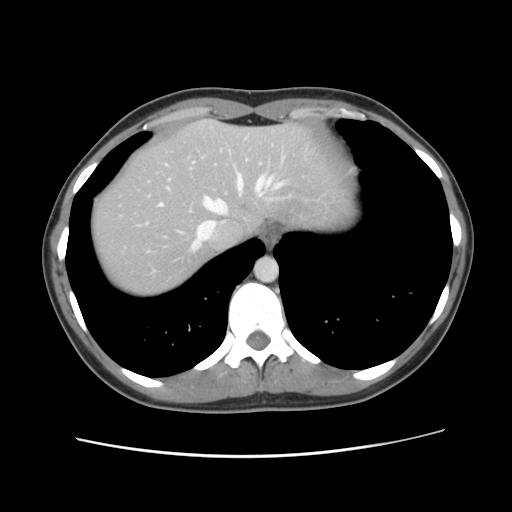
Contrast-enhanced abdominal CT, one axial slice. Position 103 of 134 along the scan axis. 120 kVp. Intravenous contrast given. Soft-tissue window (W 400 / L 40 HU). 2.5 mm slice thickness. 512 × 512 image matrix. Female patient, age 33 years. Case-level facts recorded for this patient, not image findings: diagnosis: colorectal cancer liver metastases, imaged before liver resection; multiple liver metastases: yes; largest metastasis: 4.5 cm; disease in both lobes: yes.
Outlined on this slice (expert manual segmentation):
- hepatic veins: bounding box <160,174,285,250> (left, top, right, bottom; pixels)
- liver: <90,120,338,297>
- planned liver remnant (the part of the liver to remain after resection): <91,121,338,297>